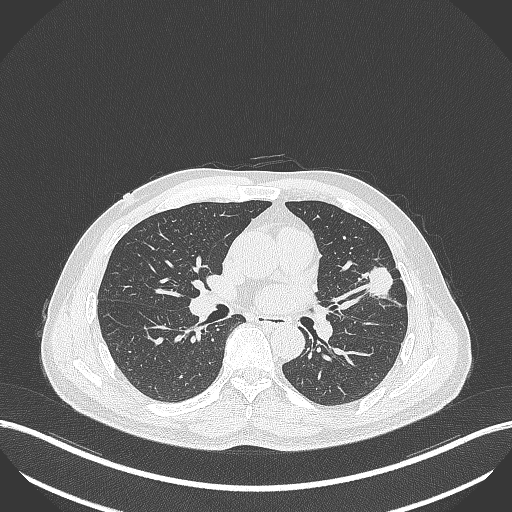
Chest CT, one axial slice; position 214 of 418 along the scan axis; reconstruction kernel B70f; lung window (W 1500 / L -600 HU); 1 mm slice thickness; 512 × 512 image matrix, field of view 400 × 400 mm. Male patient, age 55 years. Case-level facts recorded for this patient, not image findings: clinical TNM (as recorded): T1c N0 M0.
Annotated regions visible in this slice (rectangle marked by the reading radiologist):
- lung tumour (recorded histology: adenocarcinoma): box from (x=362, y=263) to (x=396, y=302) px